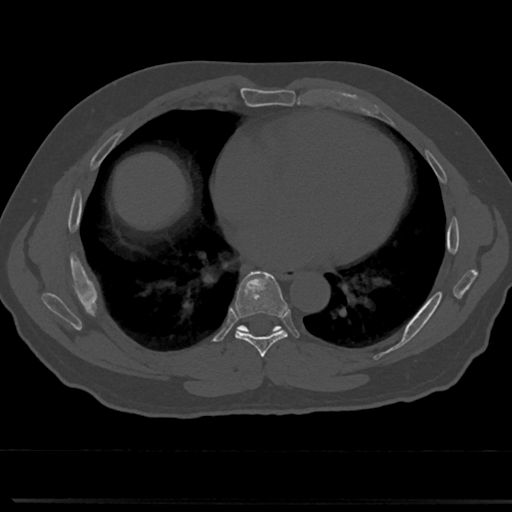
CT including the spine, one axial slice; slice 393 of 817 in the series (ordered by position); reconstruction kernel Br40s/3; bone window (W 1800 / L 400 HU); 0.5 mm slice thickness; 512 × 512 image matrix, field of view 355 × 355 mm. Male patient, age 61 years. From the clinical record (not read from this slice): primary cancer: prostate.
Structures marked on this image (semi-automatic segmentation, software-assisted and operator-edited):
- T6 vertebra: box from (x=260, y=355) to (x=269, y=377) px
- T7 vertebra: (x=214, y=275)–(x=310, y=357)